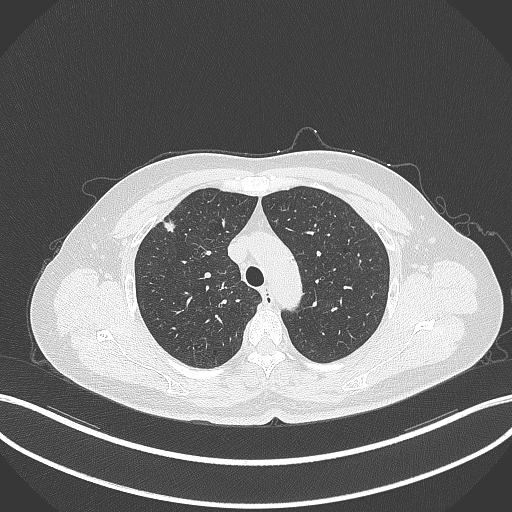
Chest CT, one axial slice. Position 277 of 353 along the scan axis. 120 kVp. Lung window (W 1500 / L -600 HU). 512 × 512 image matrix, field of view 400 × 400 mm. Patient: female, 56 years. From the clinical record (not read from this slice): clinical TNM (as recorded): T1c N0 M0.
Structures marked on this image (bounding box drawn by a radiologist):
- lung tumour (recorded histology: adenocarcinoma): bounding box [x1, y1, x2, y2] px = [160, 218, 181, 237]